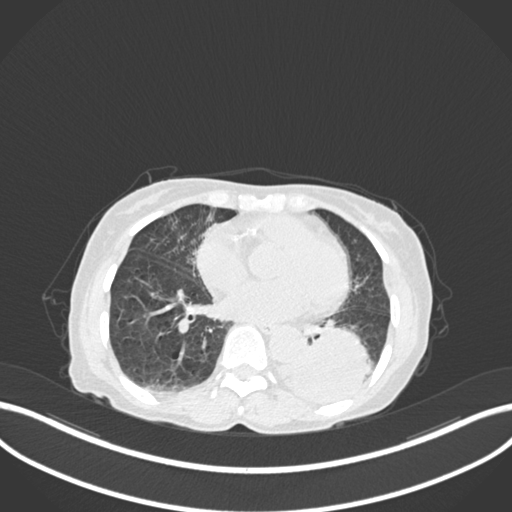
Chest CT, one axial slice. Position 52 of 233 along the scan axis. Reconstruction kernel B30f. 120 kVp. Lung window (W 1500 / L -600 HU). 1 mm slice thickness. 512 × 512 image matrix. Patient: female, 78 years. From the clinical record (not read from this slice): clinical TNM (as recorded): T3 N0 M1.
Outlined on this slice (rectangle marked by the reading radiologist):
- lung tumour (recorded histology: squamous cell carcinoma): bounding box <283,322,376,407> (left, top, right, bottom; pixels)